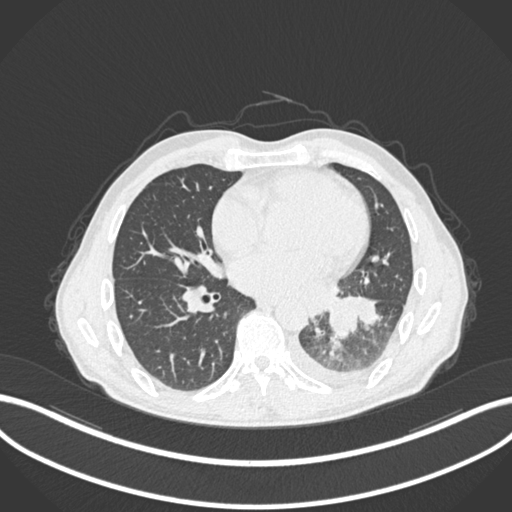
Chest CT, one axial slice; position 104 of 222 along the scan axis; reconstruction kernel B30f; 120 kVp; lung window (W 1500 / L -600 HU); 512 × 512 image matrix, field of view 400 × 400 mm. Male patient, age 47 years. From the clinical record (not read from this slice): clinical TNM (as recorded): T3 N1 M1c.
Outlined on this slice (rectangle marked by the reading radiologist):
- lung tumour (recorded histology: small cell carcinoma): bounding box <329,293,361,338> (left, top, right, bottom; pixels)